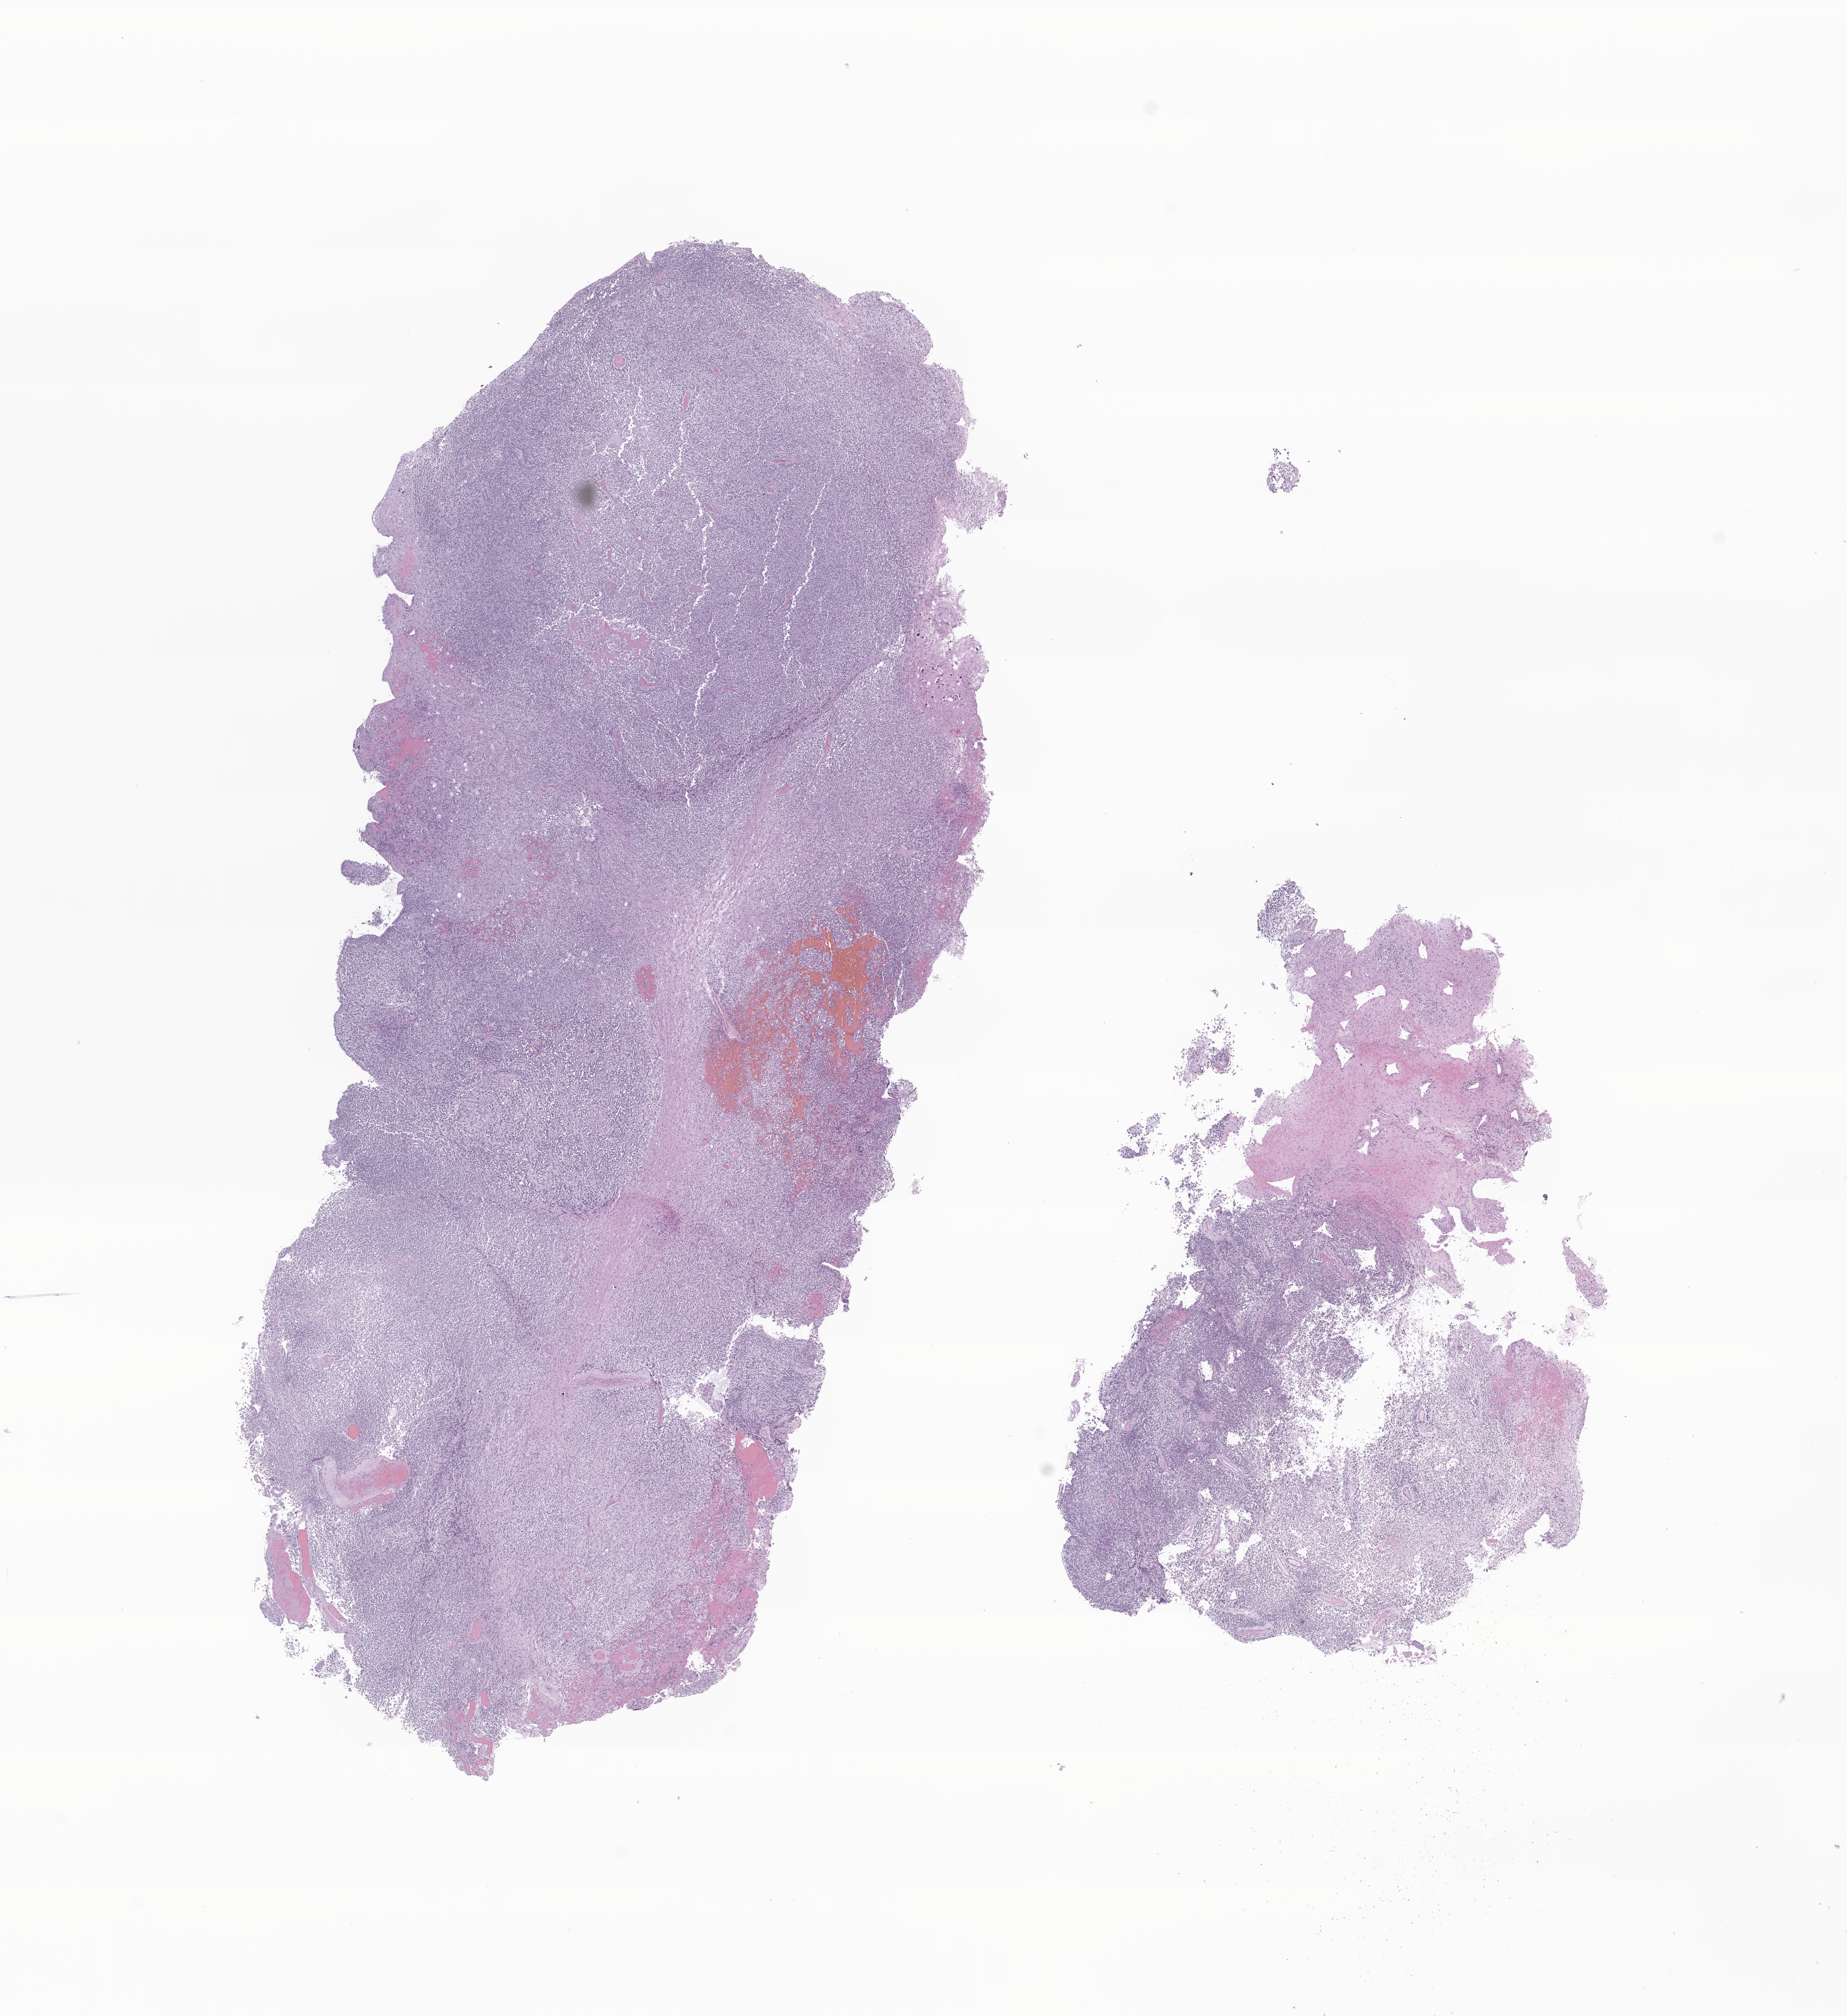
H&E whole-slide image of tumor tissue from the temporal lobe — a low-resolution overview of the entire scanned area, about 14.5 x 15.8 mm, formalin-fixed, paraffin-embedded (FFPE) tissue. Patient: female, age 36 months (3 years).
Recorded diagnosis: Neuroblastoma, NOS.